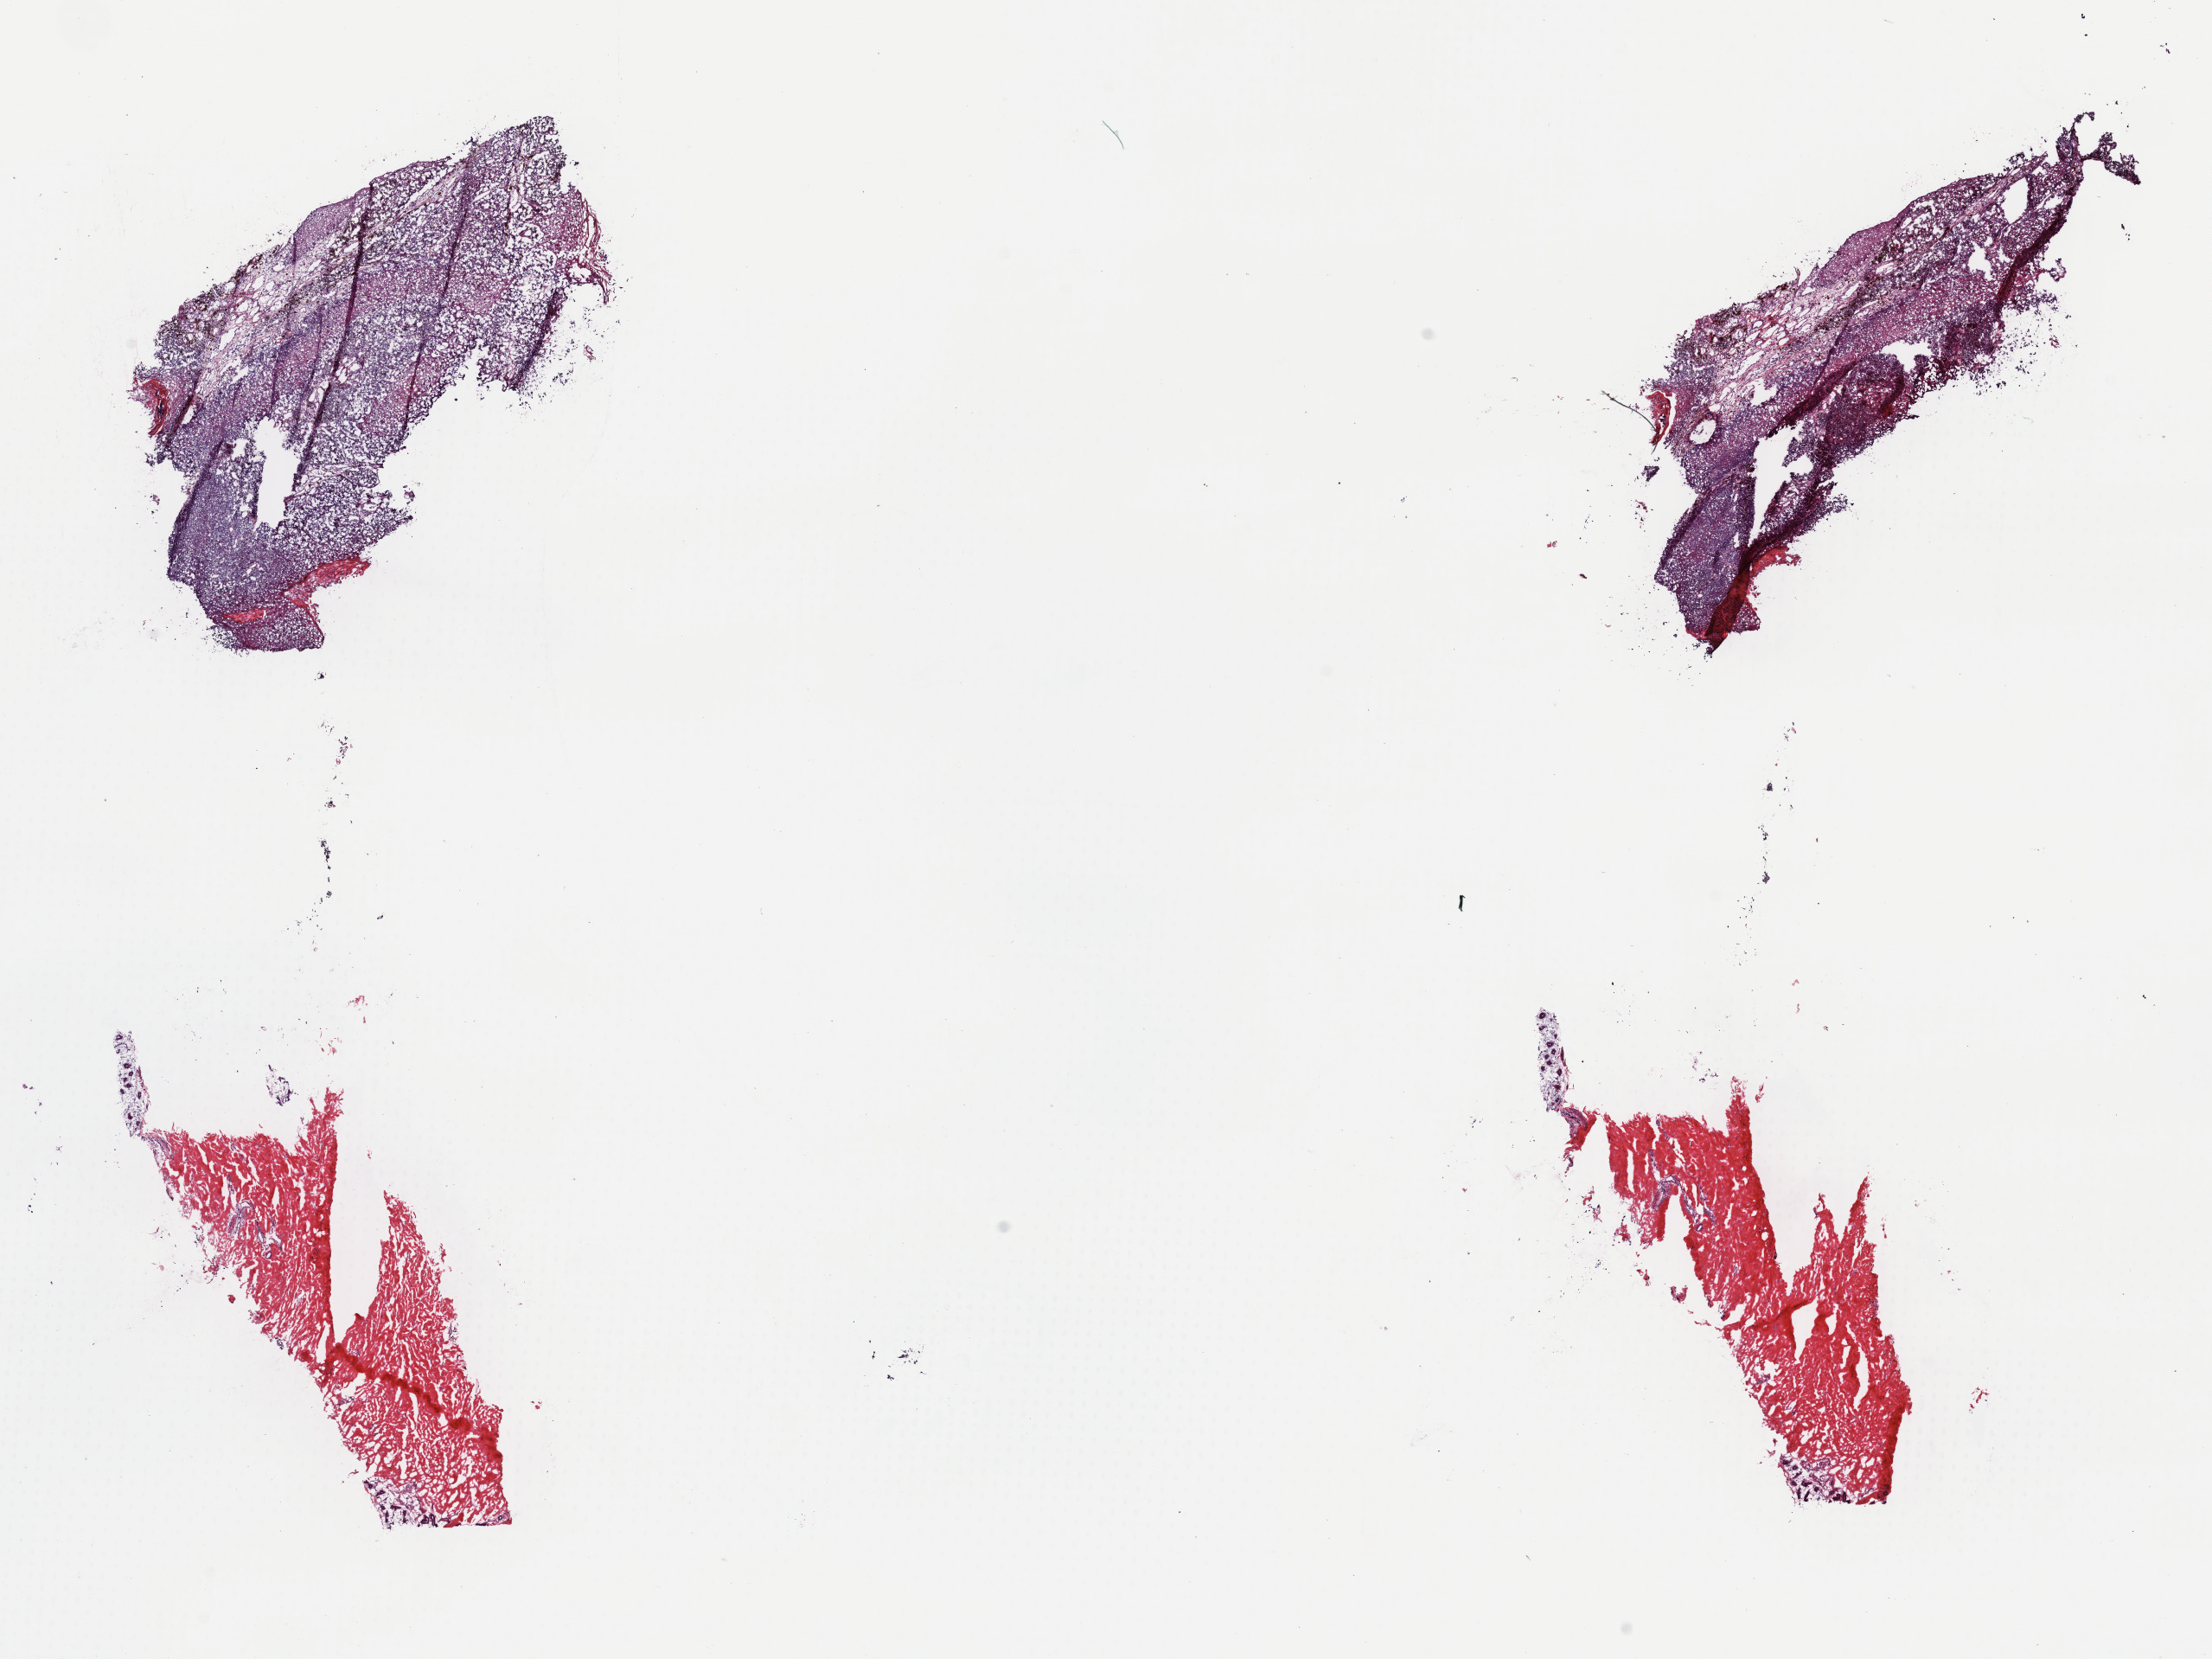
Digitized Hematoxylin and eosin (H&E) stained tissue section (whole slide), a low-resolution overview of the entire scanned area, about 20.2 x 15.1 mm (acquisition: 40x scan), frozen section from the top of the tissue portion, primary tumour sample from the skin. Female, age 42 years at initial diagnosis. Composition of this section per pathologist review: tumour cells 60%, tumour nuclei 75%, normal cells 40%, stromal cells 0%, necrosis 0%. Infiltration values recorded for this section: lymphocyte infiltration 2%, monocyte infiltration 0%, neutrophil infiltration 0%.
* diagnosis: Malignant melanoma, NOS
* AJCC pathologic stage: IIIB